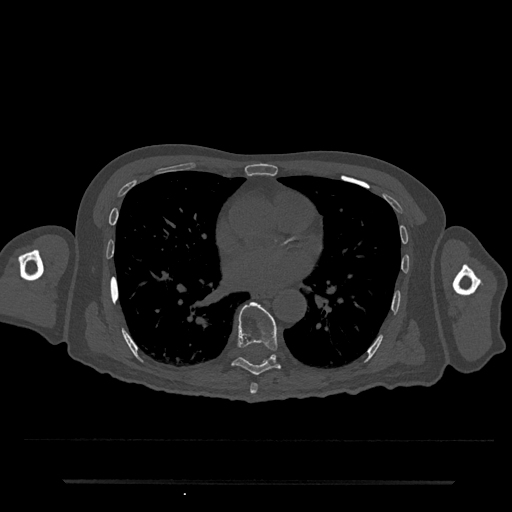
CT including the spine, one axial slice; slice 420 of 797 in the series (ordered by position); reconstruction kernel Br40s/3; 120 kVp; bone window (W 1800 / L 400 HU); 0.5 mm slice thickness; 512 × 512 image matrix, field of view 427 × 427 mm. Male patient, age 74 years. From the clinical record (not read from this slice): primary cancer: prostate.
Annotated regions visible in this slice (semi-automatically segmented with operator editing):
- T7 vertebra: box from (x=250, y=383) to (x=258, y=394) px
- T8 vertebra: (x=232, y=302)–(x=281, y=376)